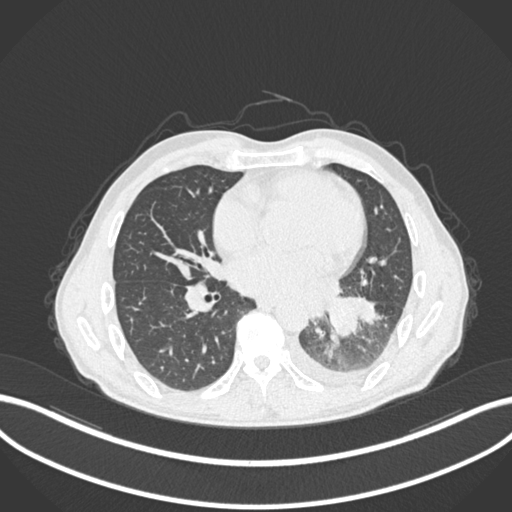
Chest CT, one axial slice. Reconstruction kernel B30f. Lung window (W 1500 / L -600 HU). 512 × 512 image matrix, field of view 400 × 400 mm. Male patient, age 47 years. Case-level facts recorded for this patient, not image findings: clinical TNM (as recorded): T3 N1 M1c.
Annotated regions visible in this slice (bounding box drawn by a radiologist):
- lung tumour (recorded histology: small cell carcinoma): bounding box (x1, y1, x2, y2) in pixels: (324, 296, 359, 338)